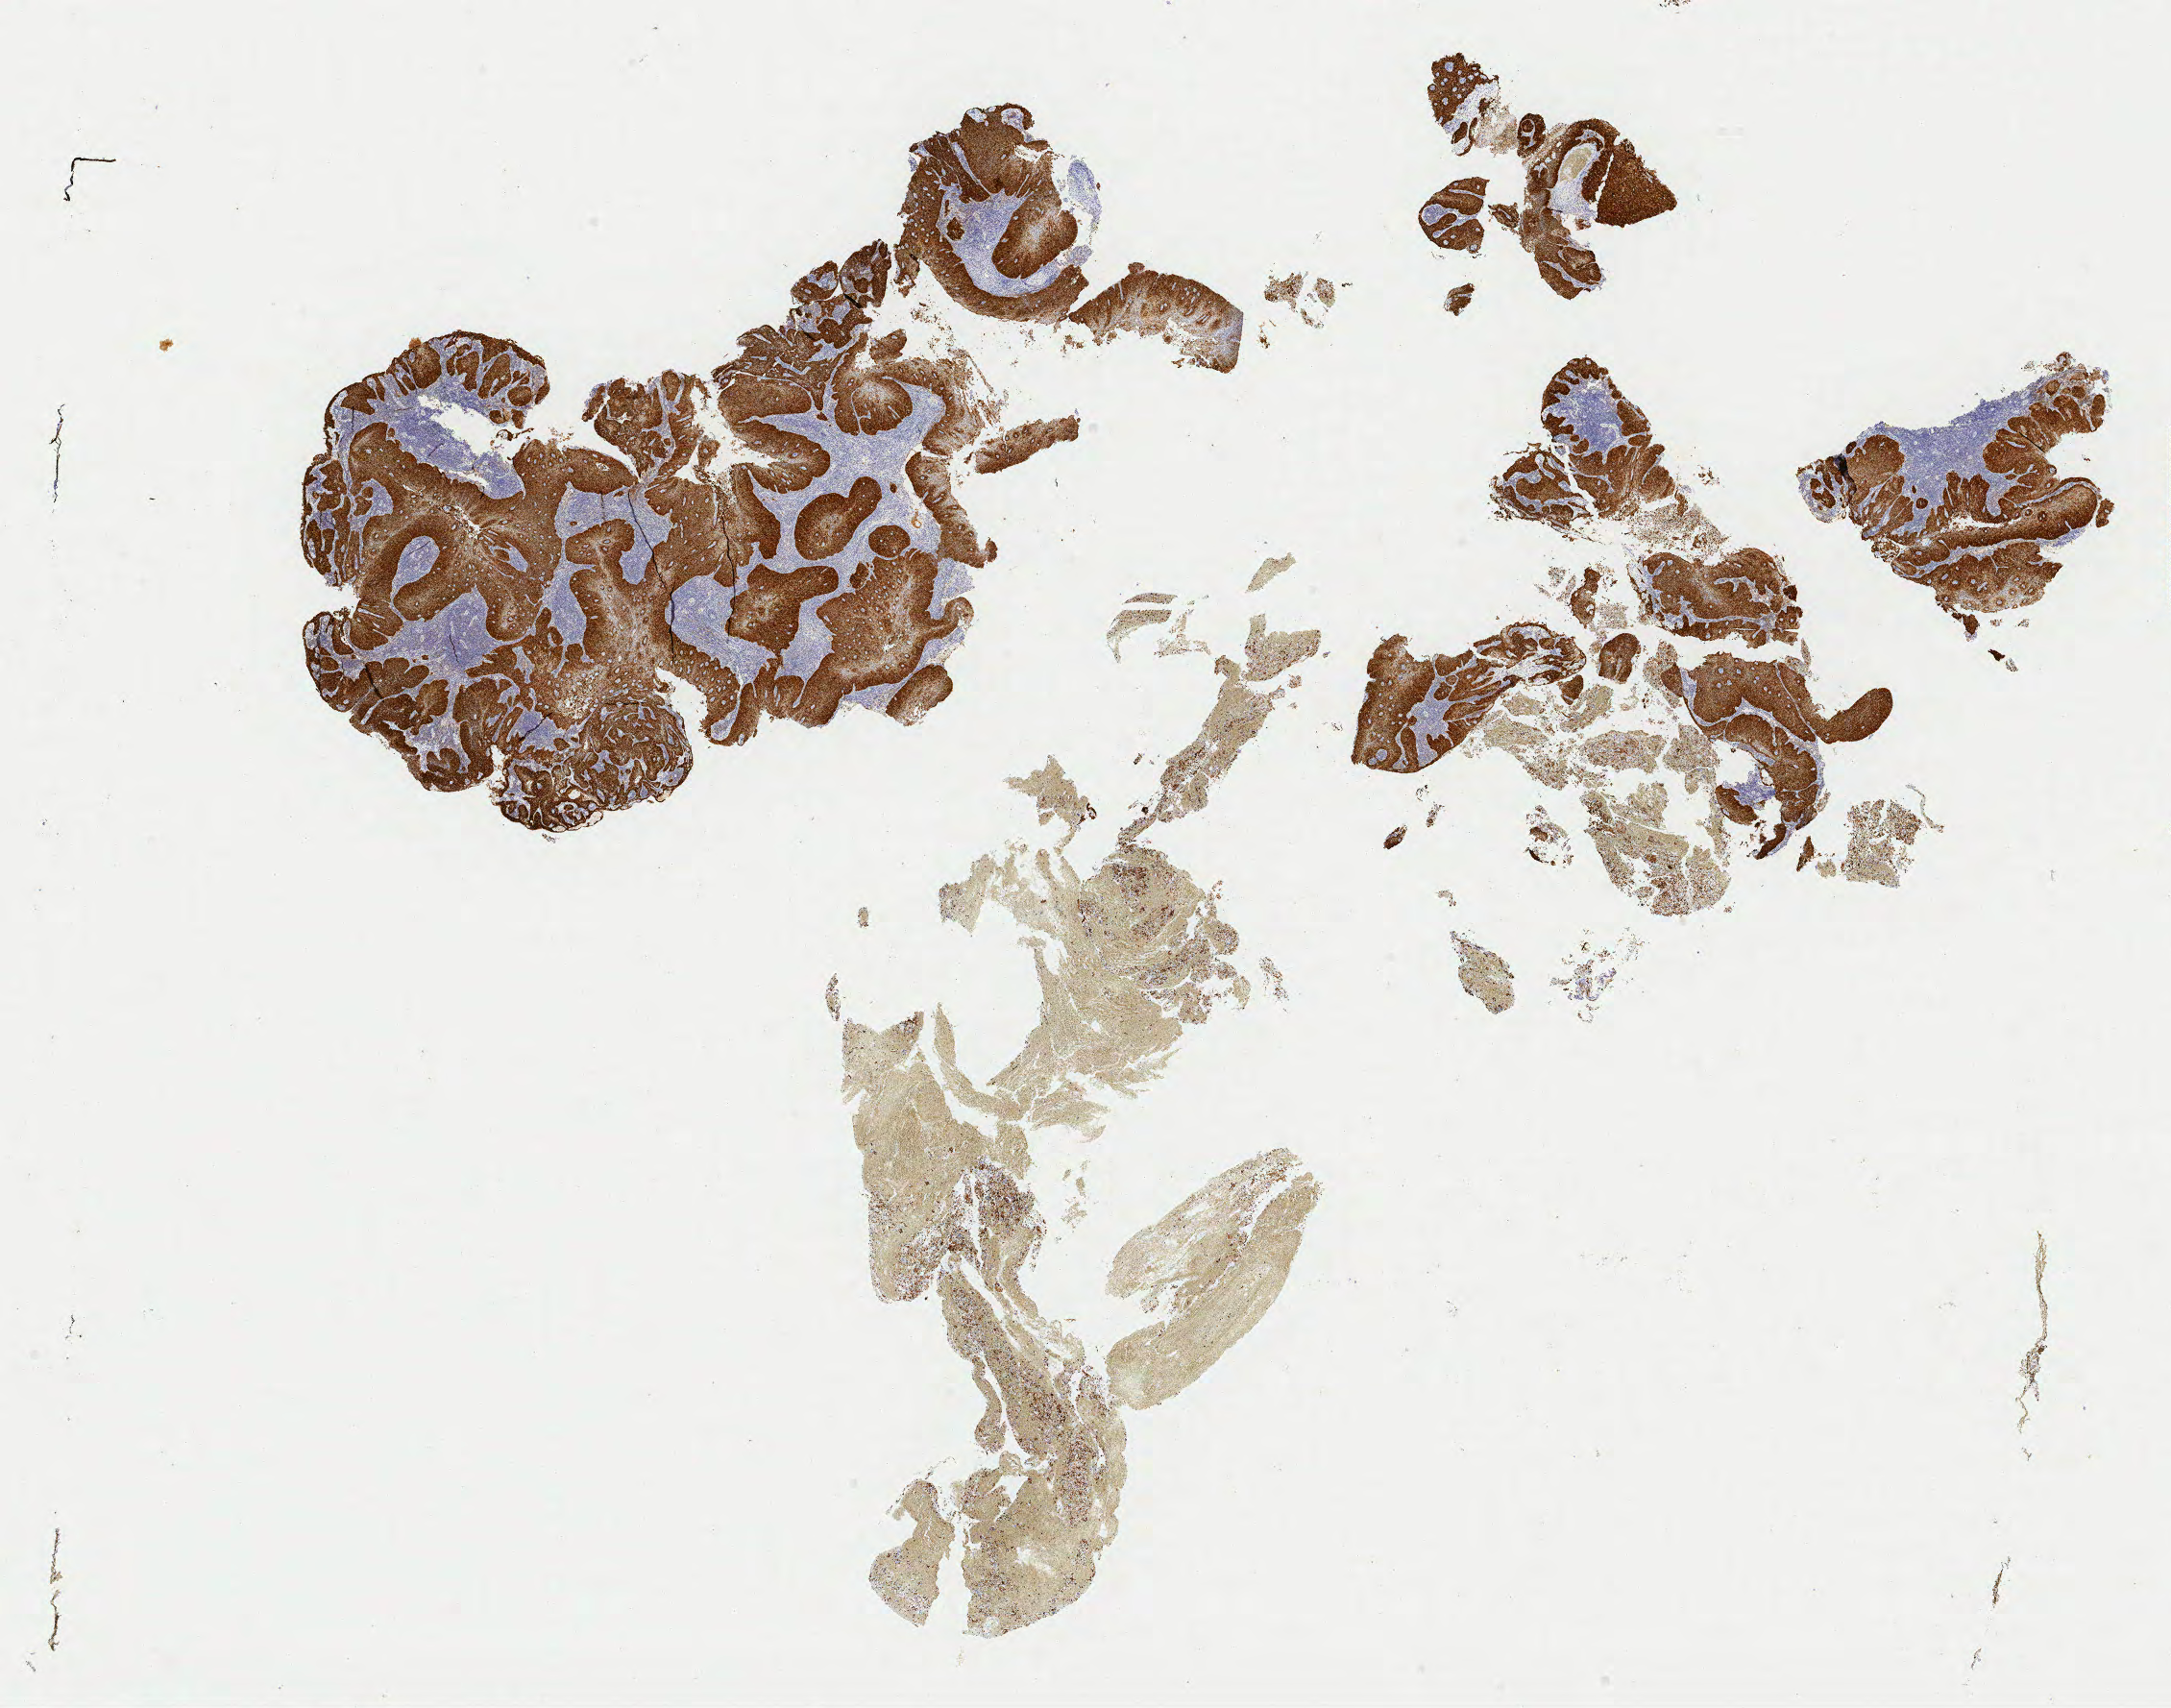
Whole-slide image, immunohistochemical stain for p16 (p16INK4a) — a low-resolution overview of the entire scanned area, about 17.9 x 14.1 mm. Specimen: tumor tissue. Anatomic site: cervix. Patient female; 47 years old.
Diagnosis: Squamous cell carcinoma, large cell, nonkeratinizing, NOS.